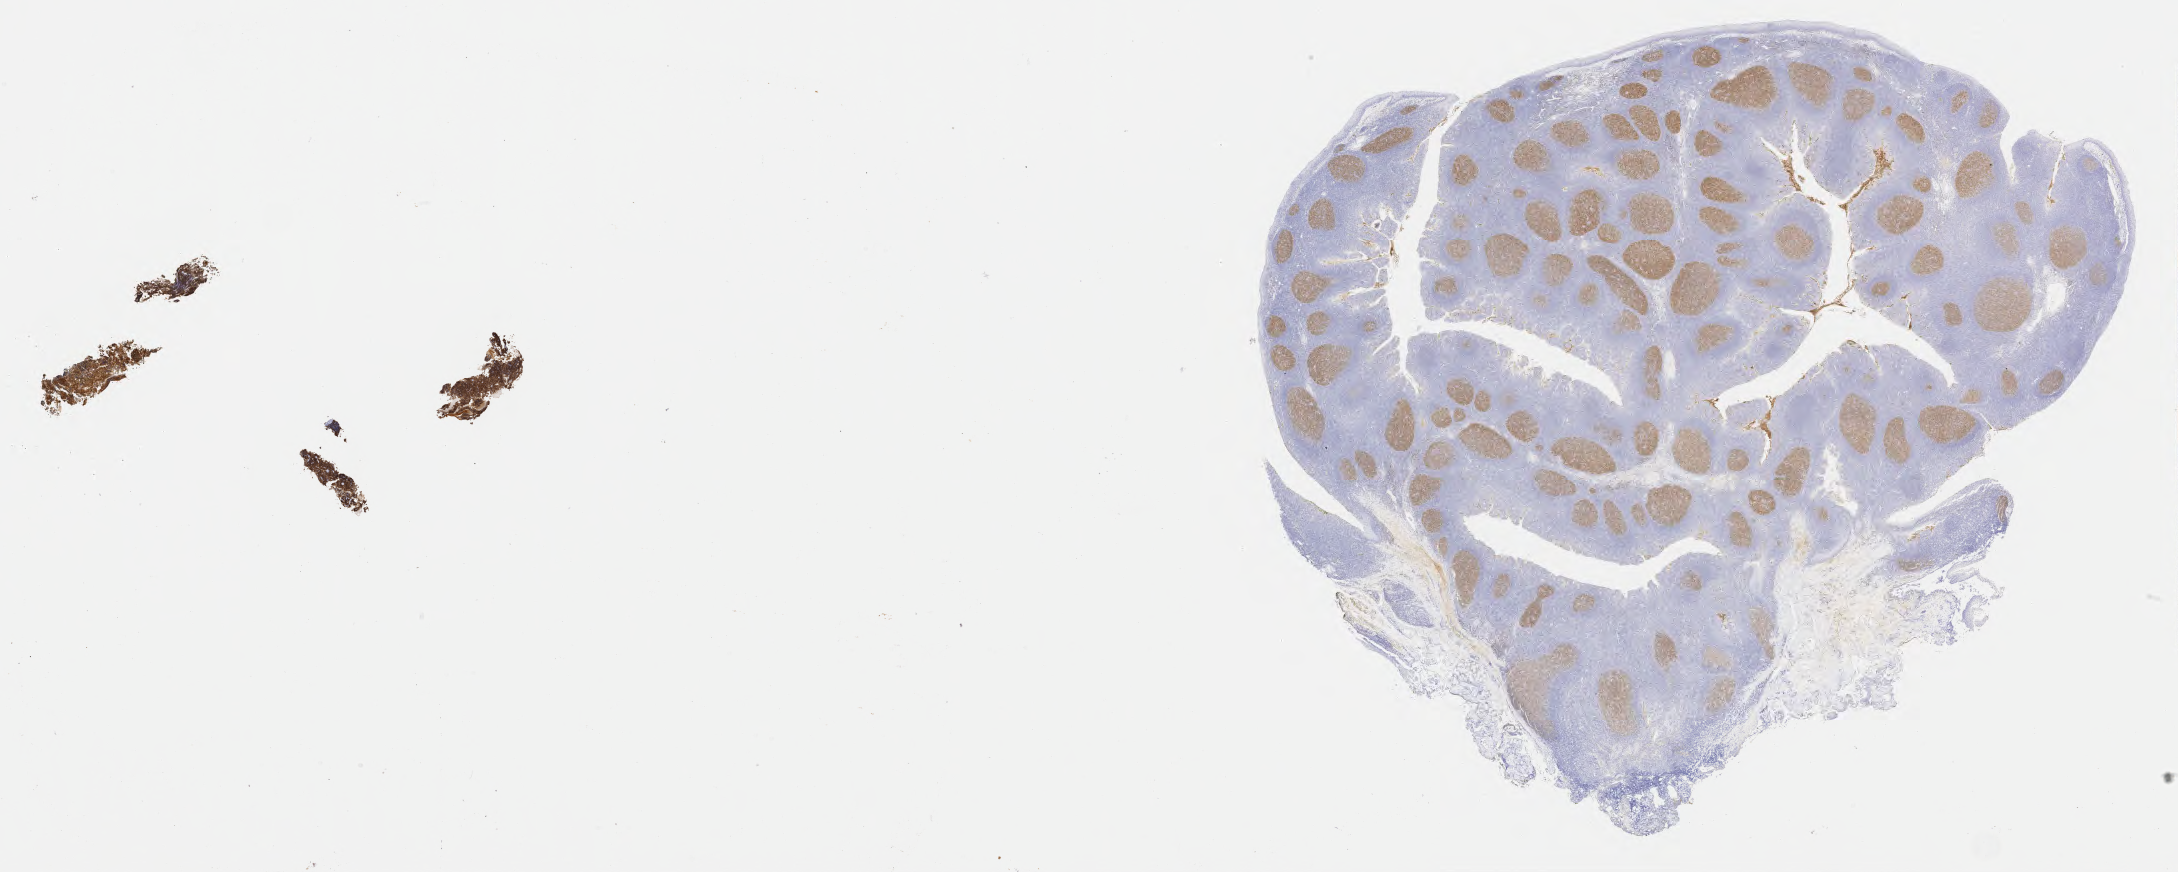
IHC for CD10, whole-slide image, a low-resolution overview of the entire scanned area, about 35.2 x 14.1 mm, specimen: tumor tissue, anatomic site: lymph node of head and neck. Female patient; age at initial diagnosis 4 years.
Histologic diagnosis: Burkitt lymphoma, NOS.